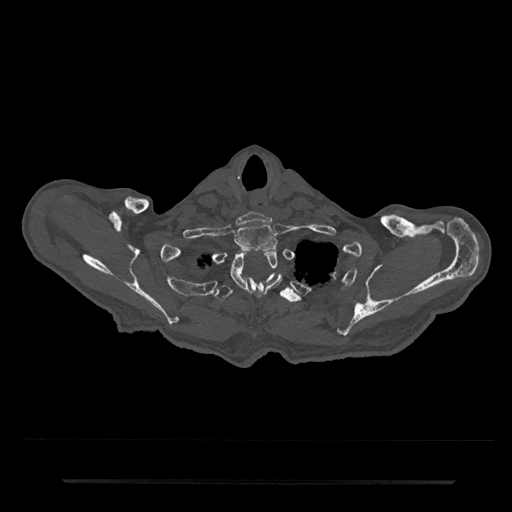
CT including the spine, one axial slice. Slice 692 of 797 in the series (ordered by position). Reconstruction kernel Br40s/3. Bone window (W 1800 / L 400 HU). 0.5 mm slice thickness. 512 × 512 image matrix, field of view 427 × 427 mm. Patient: male, 74 years. Case-level facts recorded for this patient, not image findings: primary cancer: prostate.
Structures marked on this image (semi-automatically segmented with operator editing):
- T1 vertebra: bounding box (x1, y1, x2, y2) in pixels: (234, 223, 279, 253)
- T2 vertebra: (231, 250, 282, 300)
- T3 vertebra: (213, 273, 302, 303)